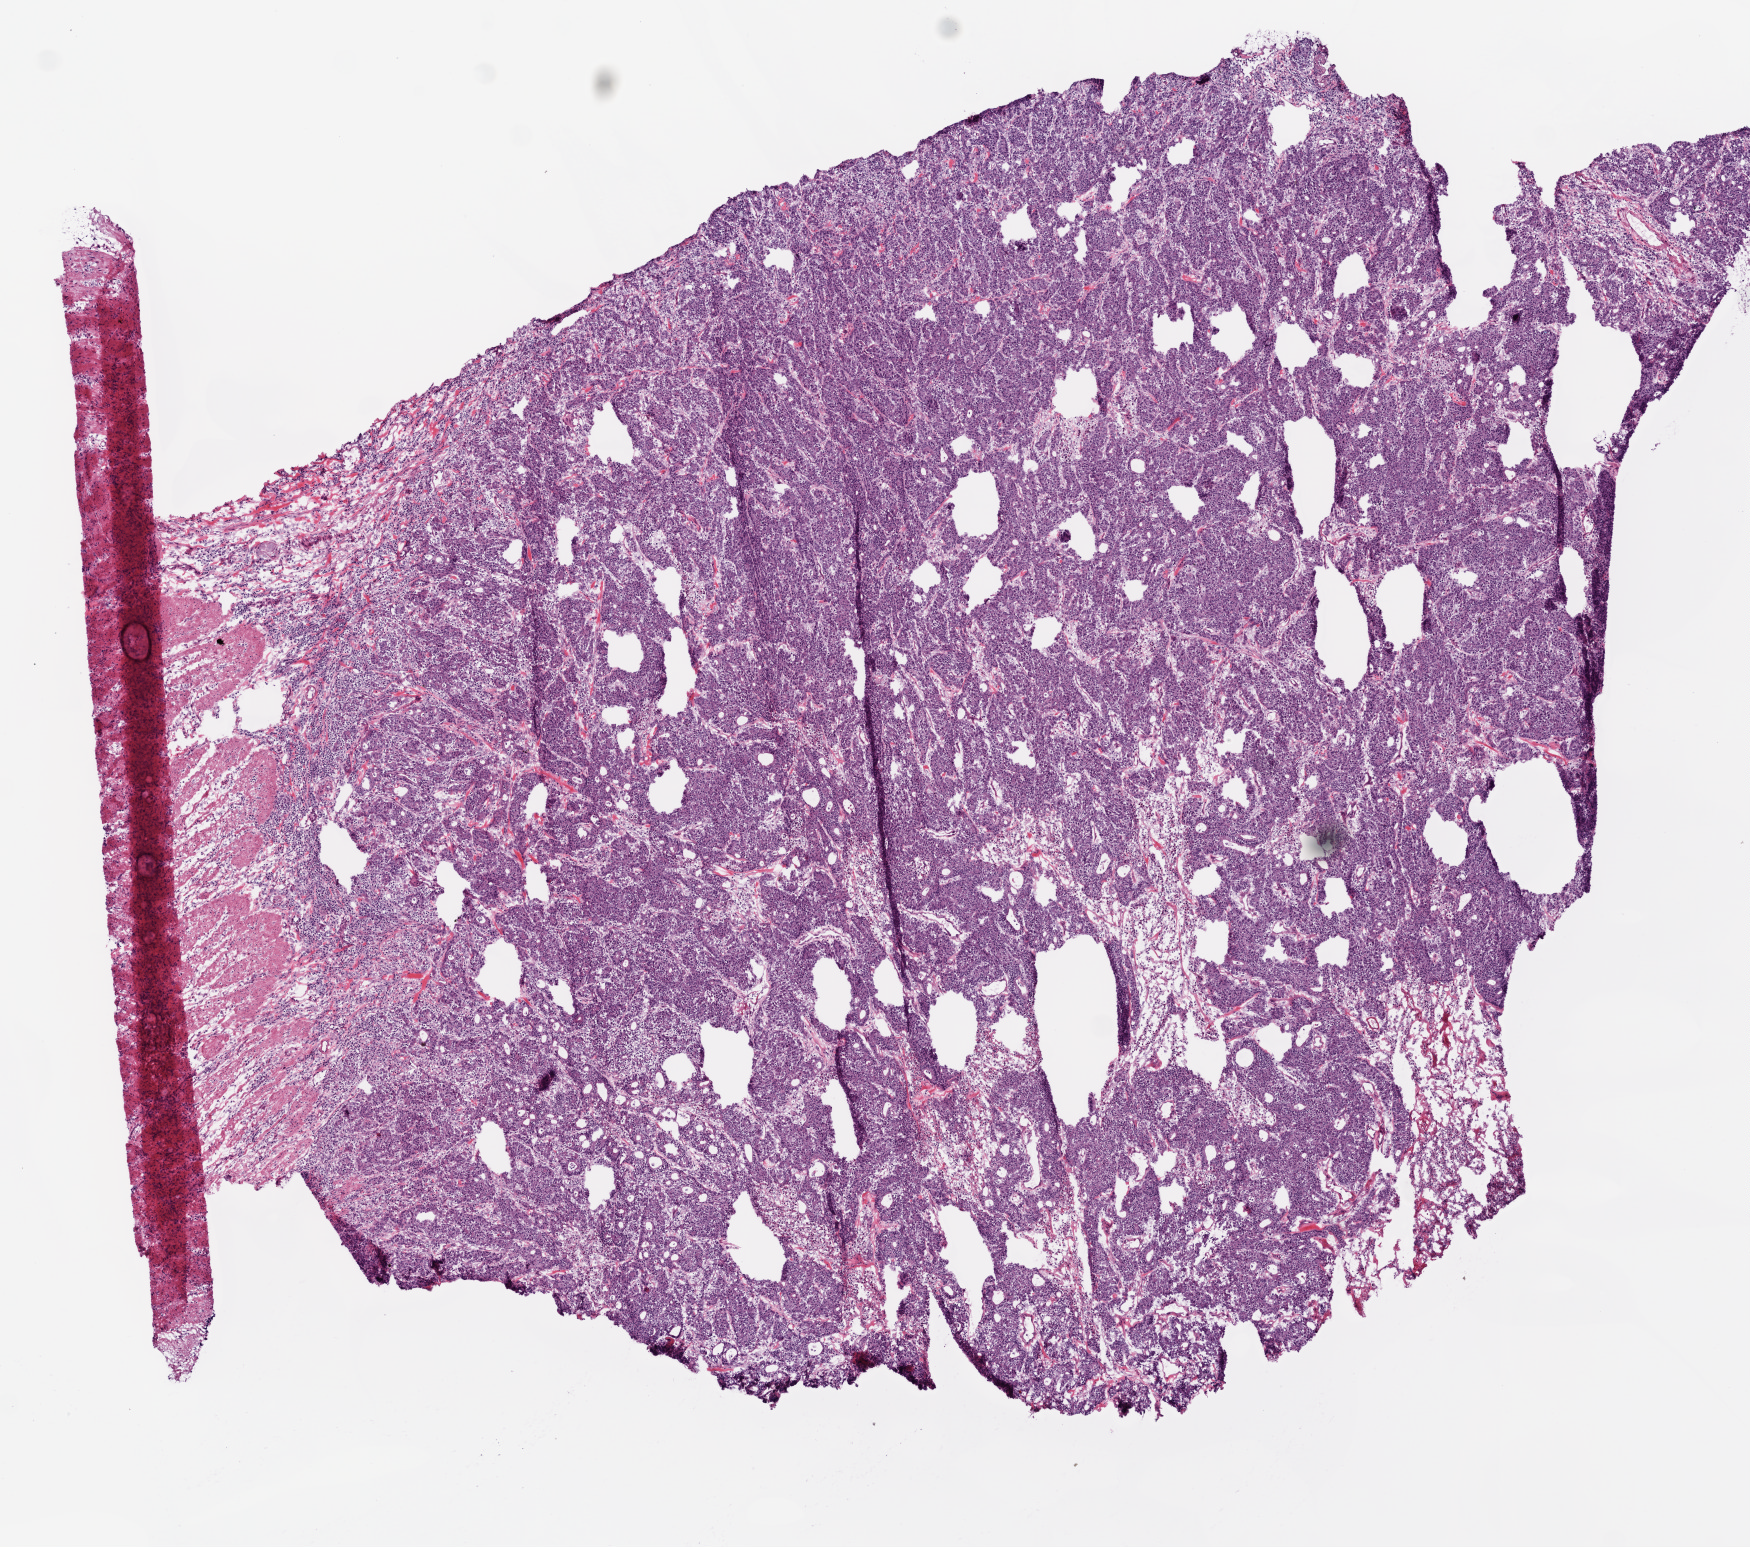
H&E-stained whole-slide image — shown as a low-resolution overview of the whole scanned area (about 7.0 x 6.2 mm, acquisition: 20x scan). Frozen section from the top of the tissue portion. Sample: primary tumour, colon. Female patient. Pathologist review of this section (percent, as recorded): tumour cells 86%, tumour nuclei 85%, normal cells 3%, stromal cells 8%, necrosis 3%.
Lymph nodes positive (case pathology): 4 of 21 examined. AJCC pathologic stage: III (5th edition). Pathologic diagnosis: Adenocarcinoma, NOS (transverse colon).